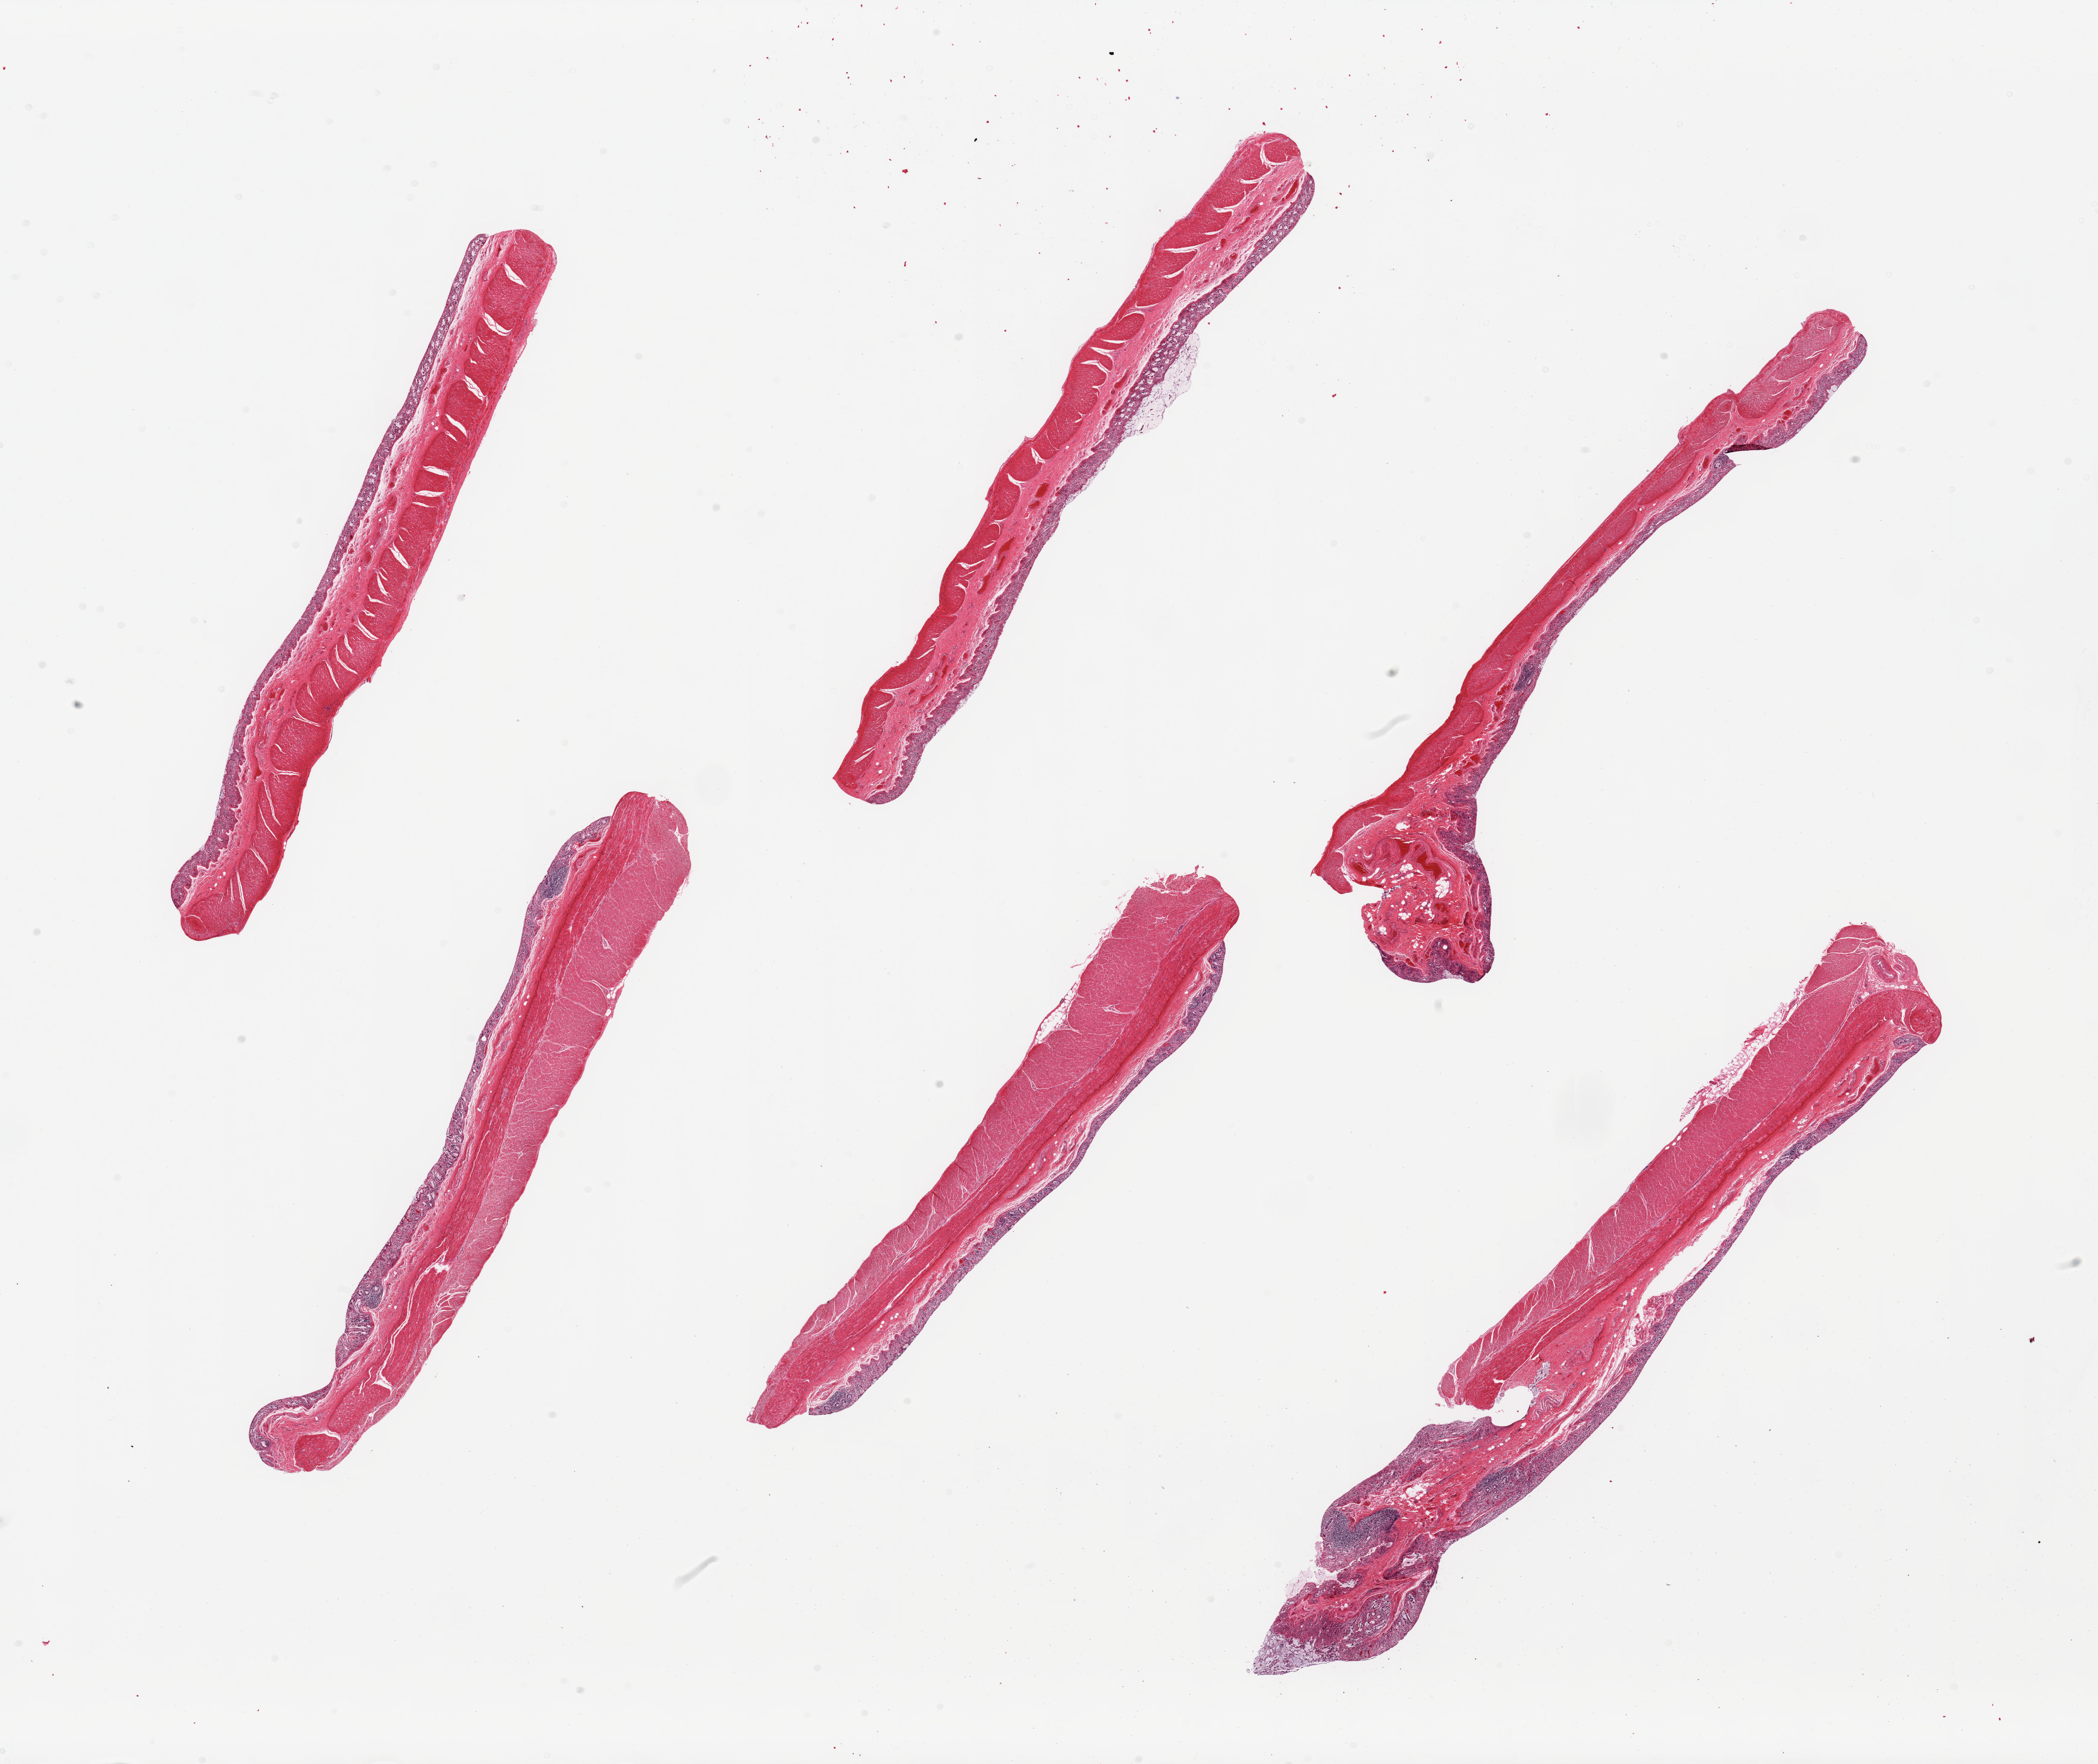
H&E whole-slide image — low-resolution overview of the scanned area, about 27.6 x 23.2 mm; PAXgene-fixed, paraffin-embedded tissue; sampled site (target tissue): transverse colon; tissue donor sample. Male donor.
Review note (as recorded): 6 pieces; mucosa severely autolyzed, muscularis intact.